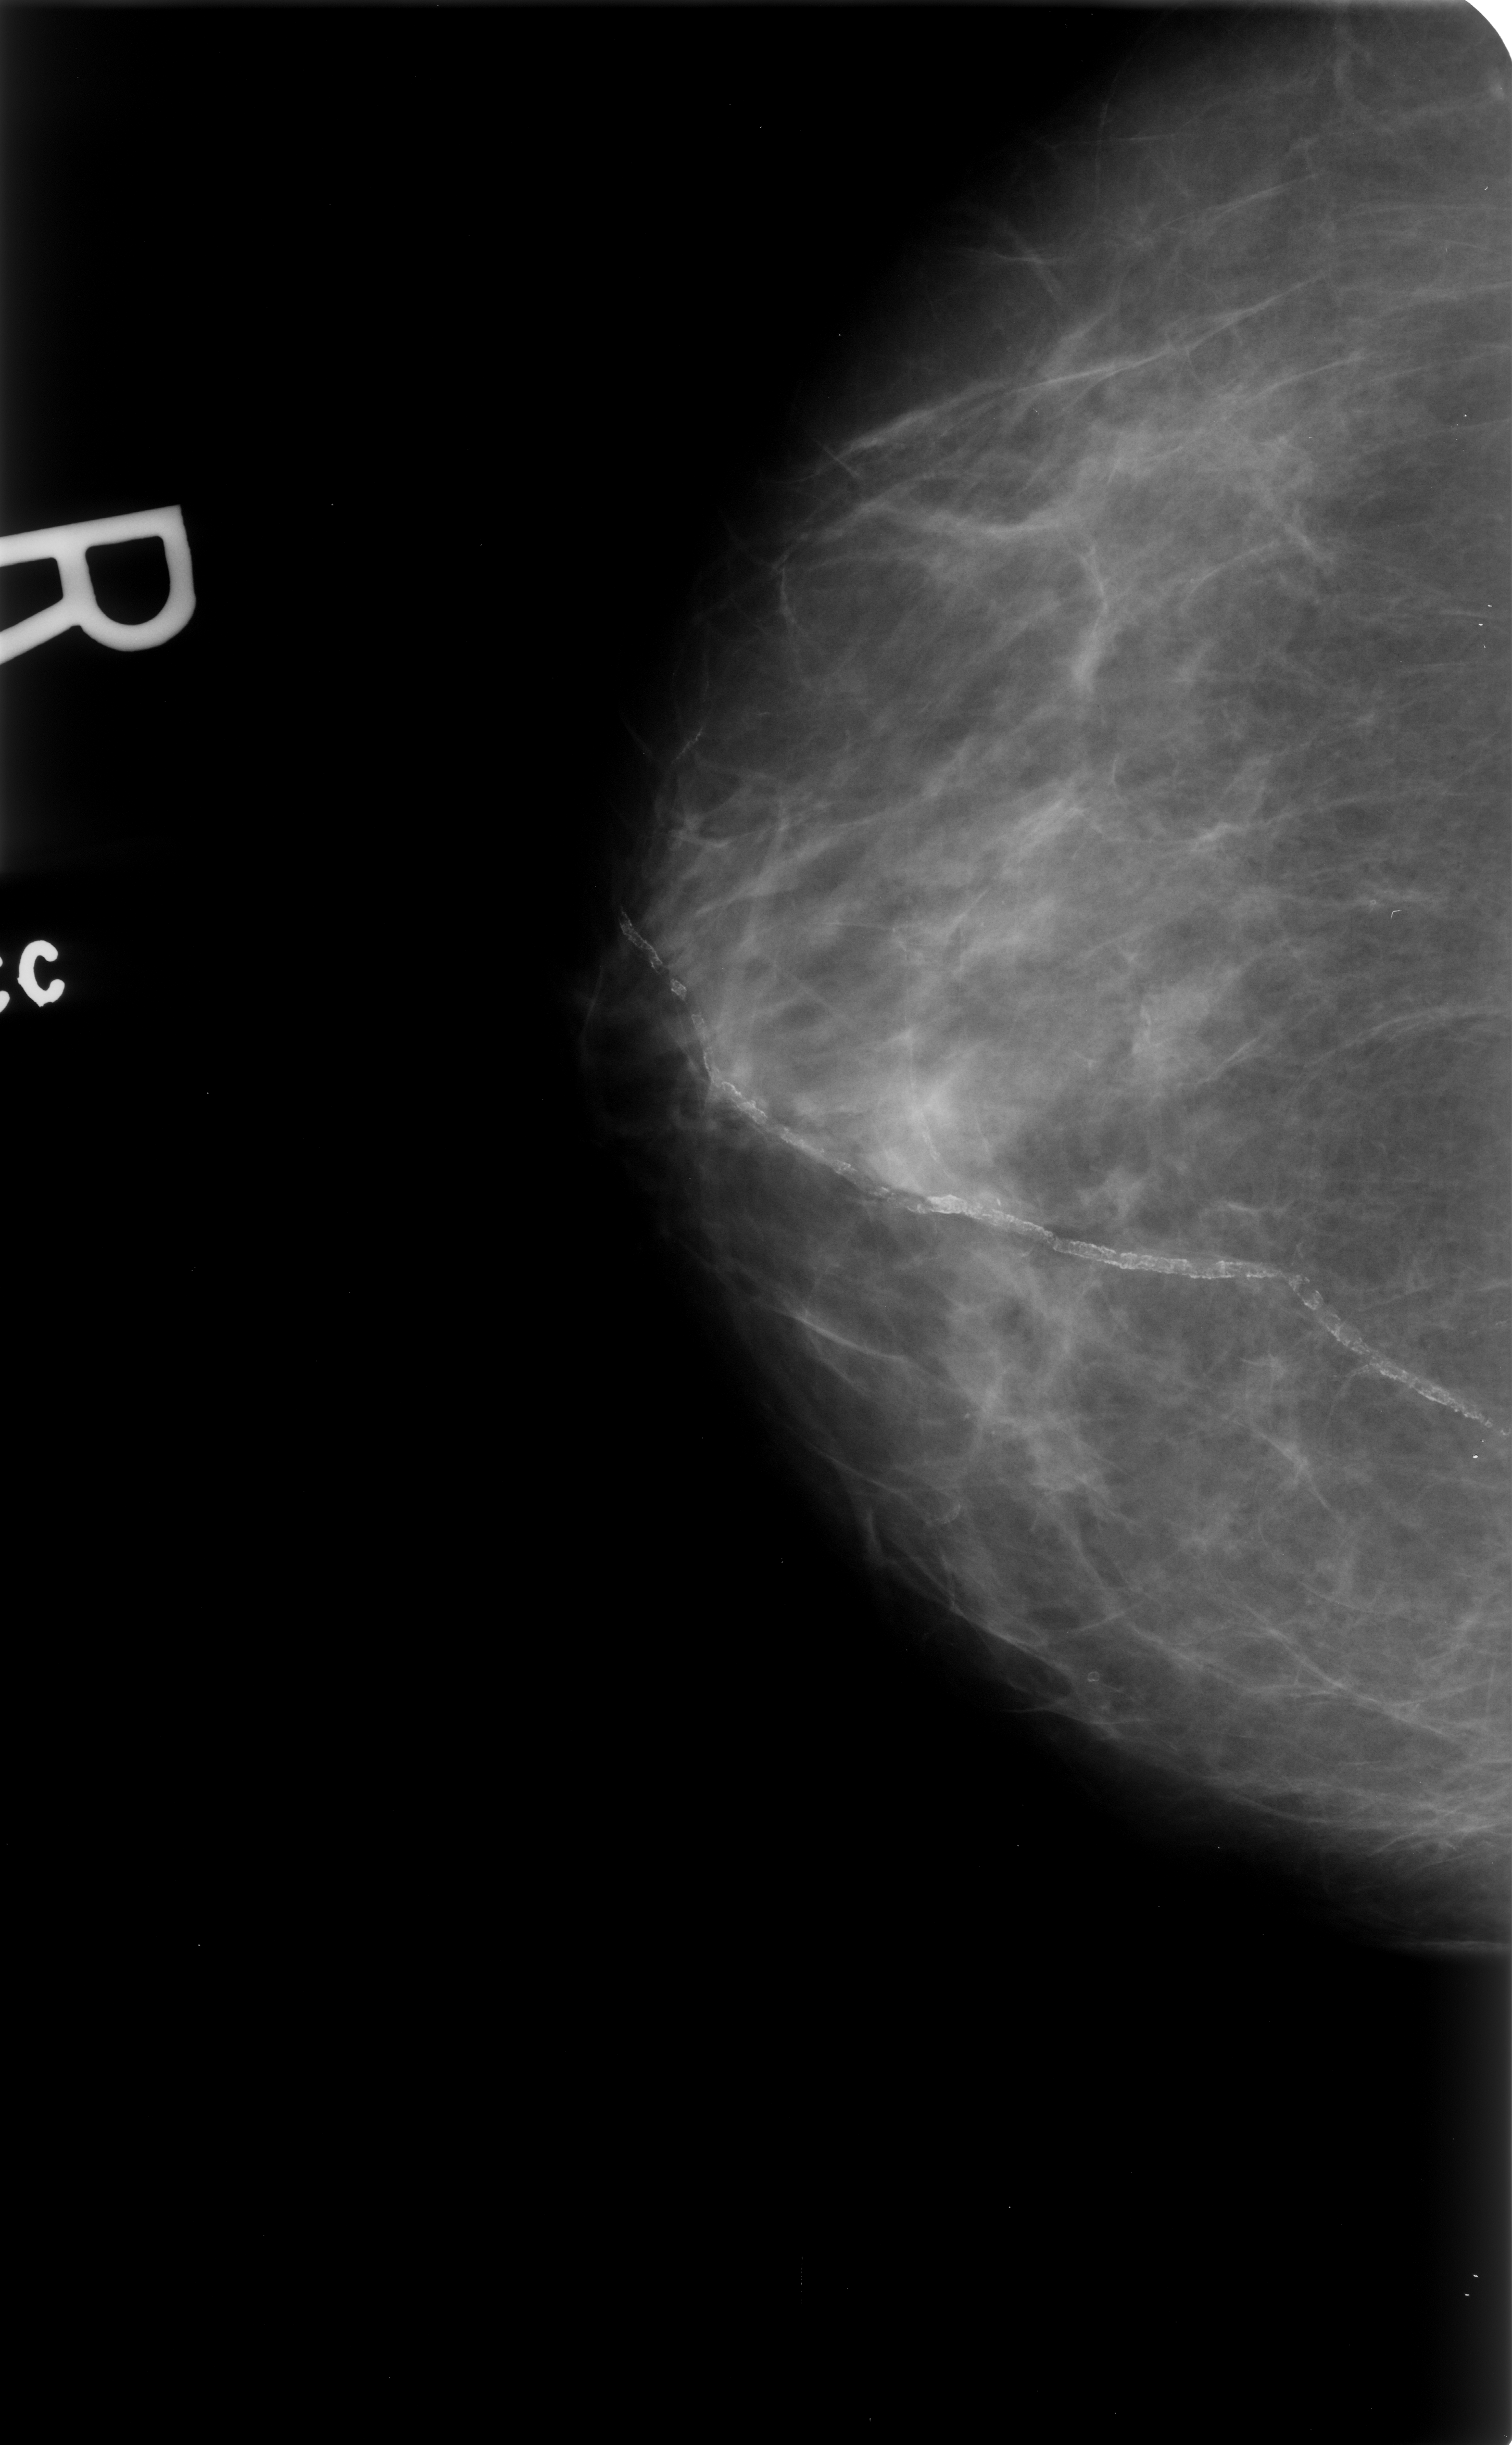
Digitized screen-film mammogram. Right breast. Craniocaudal (CC) view. Breast composition: scattered fibroglandular densities (BI-RADS density category 2 of 4). 1512 × 2445 image matrix.
Expert-marked regions of interest on this film, with their recorded descriptors:
- calcifications, morphology vascular; BI-RADS assessment category 2; outcome (as recorded, no biopsy): benign without callback (not worked up further): box from (x=653, y=958) to (x=1505, y=1459) px